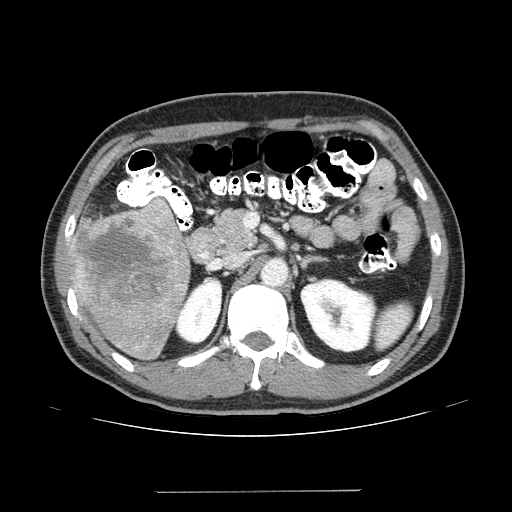
Contrast-enhanced abdominal CT (liver protocol), one axial slice. Slice 70 of 131 in the series (ordered by position). Reconstruction kernel STANDARD. 100 kVp. One of 2 acquisitions stored at this slice position. Soft-tissue window (W 400 / L 40 HU). 2.5 mm slice thickness. 512 × 512 image matrix. From the clinical record (not read from this slice): diagnosis: hepatocellular carcinoma (patient treated with transarterial chemoembolisation; whether this scan precedes or follows treatment is not stated here); TNM stage (as recorded): Stage-I; Child-Pugh class: A; tumour differentiation: poorly differentiated; tumour nodularity: uninodular.
Annotated regions visible in this slice (semi-automatic segmentation, software-assisted and operator-edited):
- liver parenchyma outside the tumour (the mass and vessels are separate outlines, so this box may not span the whole liver): bounding box [x1, y1, x2, y2] px = [70, 207, 190, 360]
- mass: [72, 195, 188, 326]